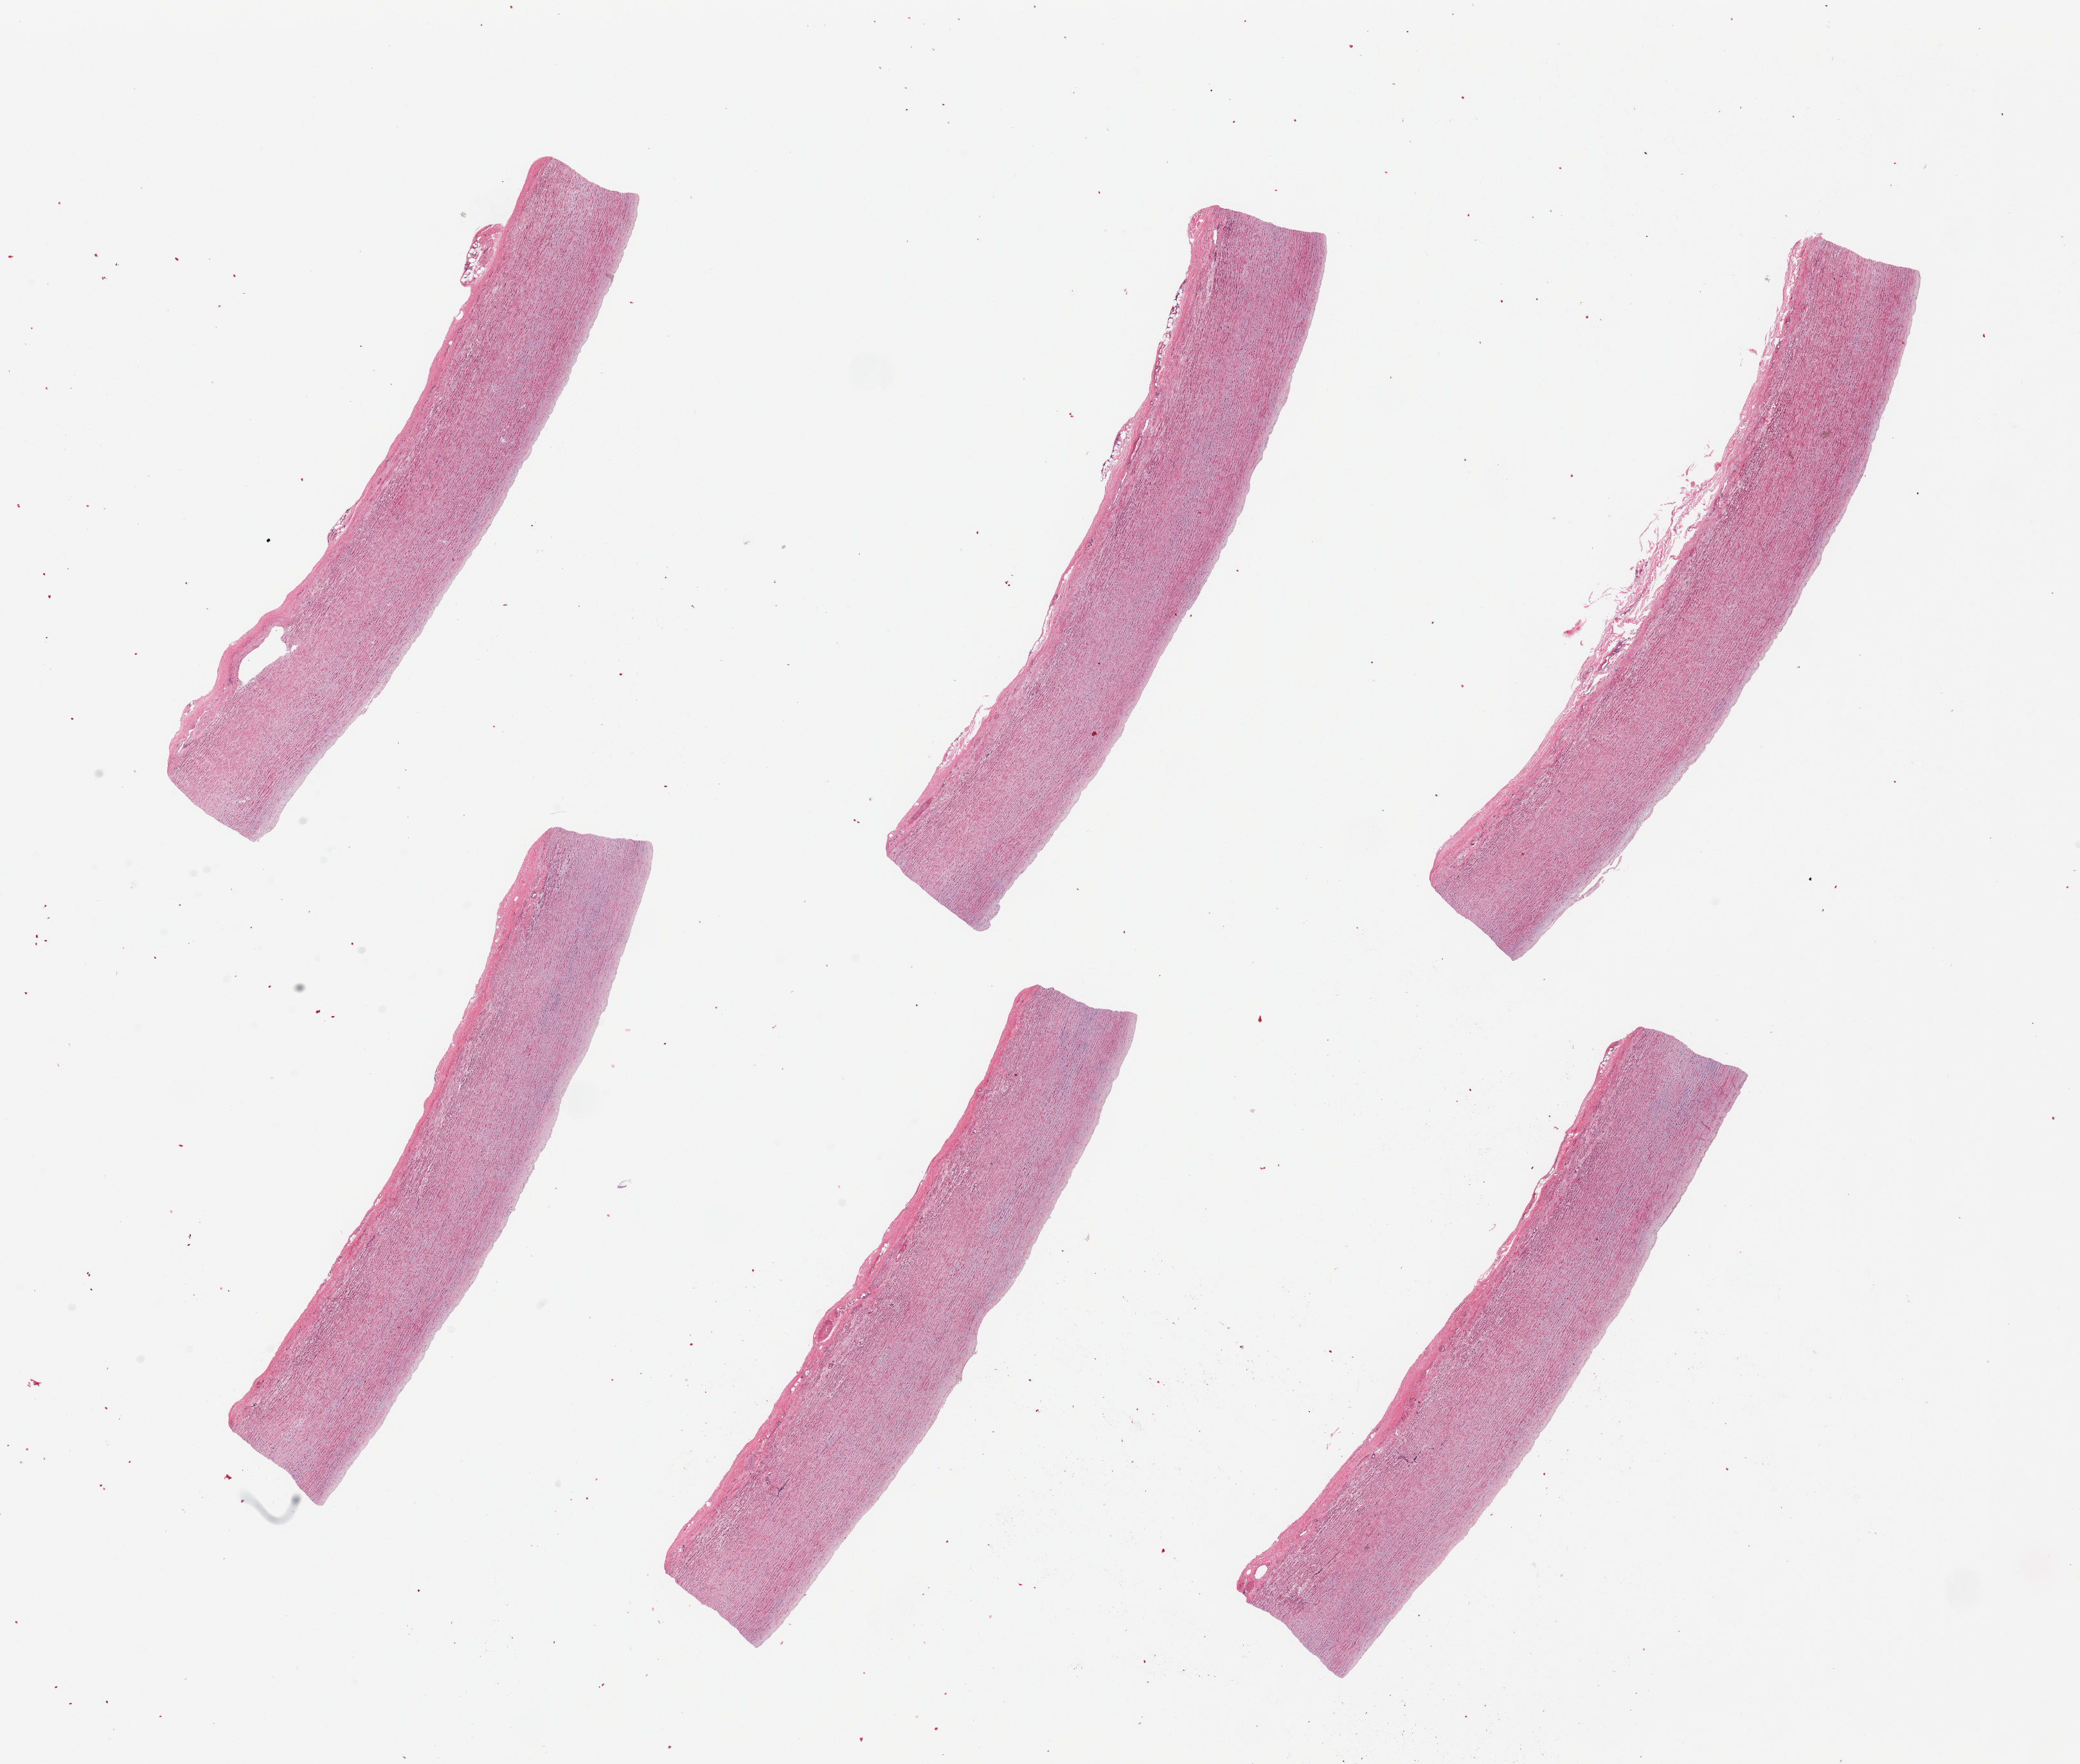
Haematoxylin and eosin whole-slide image — shown as a low-resolution overview of the whole scanned area (about 25.6 x 21.7 mm). PAXgene-fixed, paraffin-embedded tissue. Target tissue: aorta. Donor tissue sample. Donor sex: female.
Review note (as recorded): 6 pieces; trace rim of adventitia.